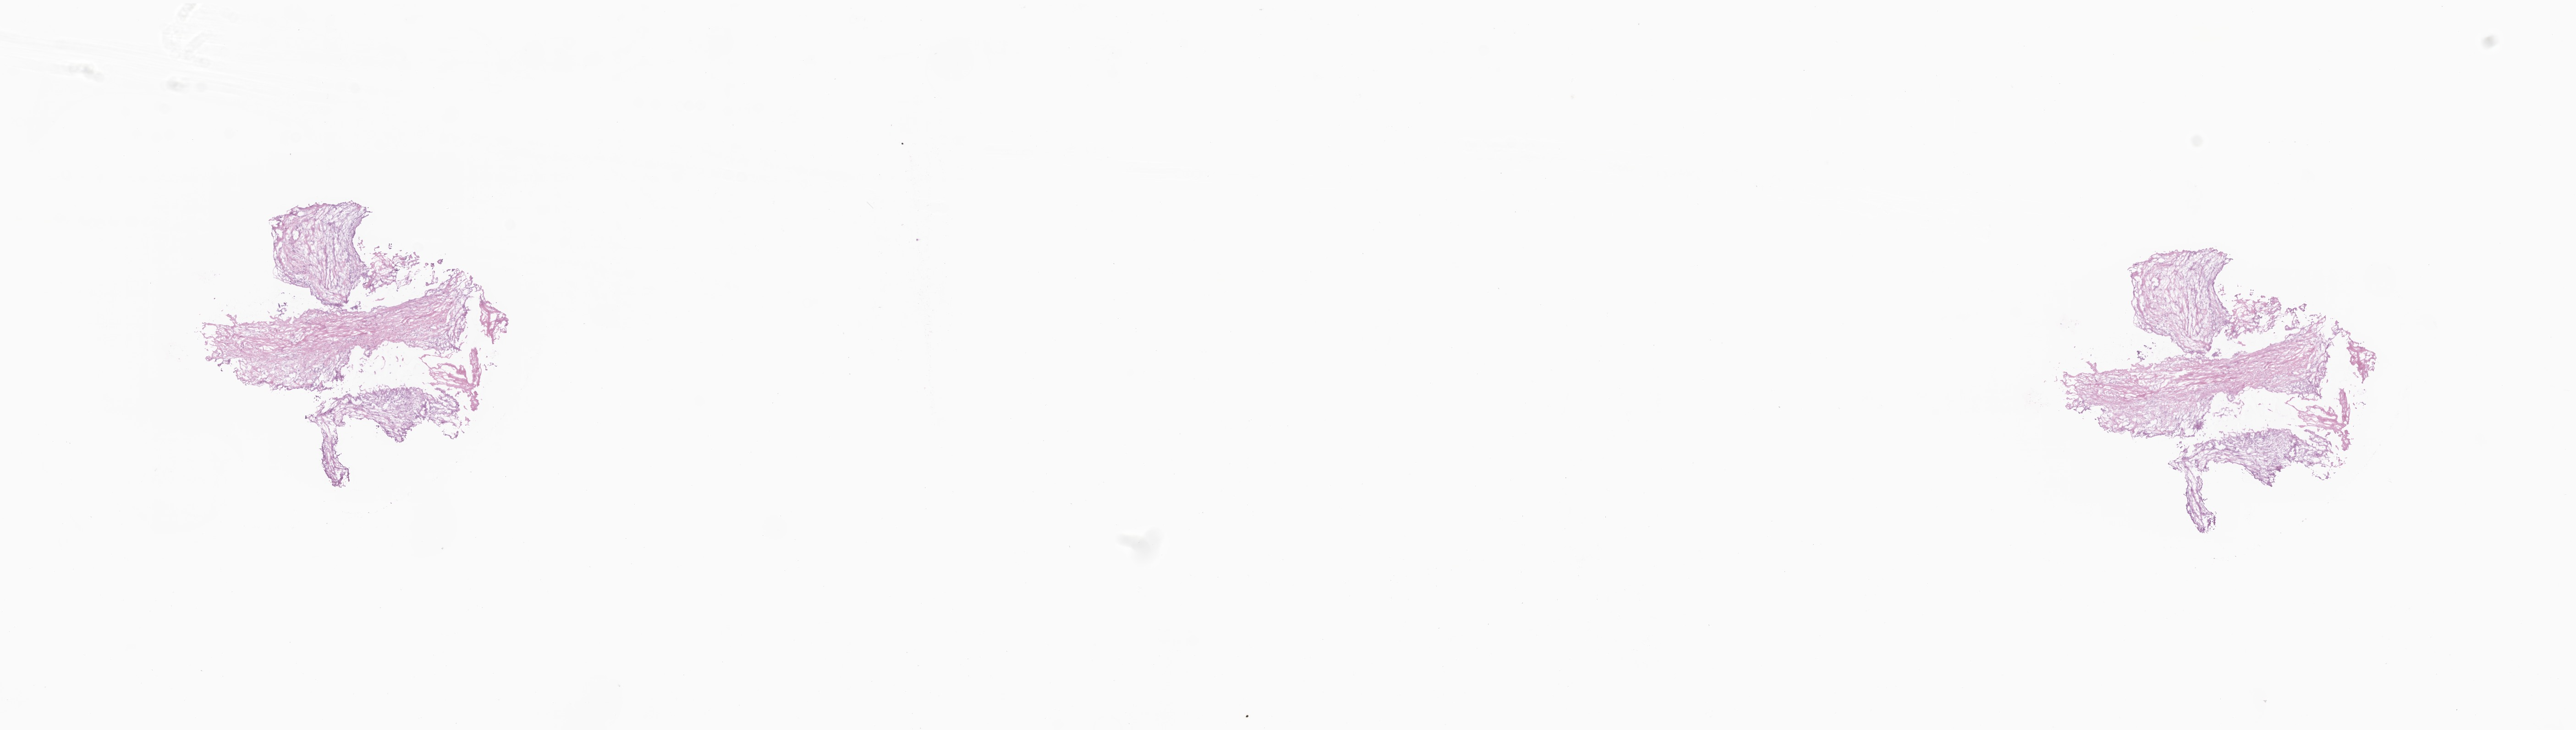
Digitized H&E-stained section — shown as a low-resolution overview of the whole scanned area (about 23.7 x 6.7 mm). Frozen section (tissue freezing medium). Specimen: metastatic tumor tissue, resected from liver. Patient: female, age at initial diagnosis 58 years. Composition of this section per pathologist review: tumor cells 18%, tumor nuclei 88%, stromal cells 80%, necrosis 2%, normal cells 0%. Infiltration values recorded for this section: lymphocyte infiltration 5%, monocyte infiltration 1%, neutrophil infiltration 0%.
Section: bottom of the tissue portion. Patient diagnosis (primary): Adenocarcinoma, NOS.